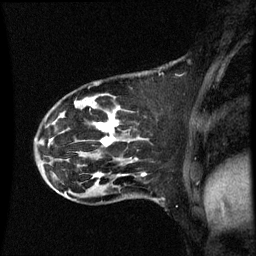
Breast MRI (dynamic contrast-enhanced), one sagittal slice. Slice 18 of 60 in the series (ordered by position). Dynamic contrast-enhanced series, image 2 of 3 at this slice position (ordered by acquisition). 1.5 T. TE 4.2 ms, TR 8.9 ms. 2 mm slice thickness. 256 × 256 image matrix, field of view 200 × 200 mm. Female patient, age 44 years. From the clinical record (not read from this slice): setting: breast cancer imaged before/during neoadjuvant chemotherapy; receptor status: HR-positive, HER2-negative.
Outlined on this slice (semi-automatic segmentation, software-assisted and operator-edited):
- analysis volume of interest (the breast-tissue region the enhancement analysis was run in; not a lesion): bounding box <43,82,149,189> (left, top, right, bottom; pixels)
- tumour enhancement mask (voxels above the 70 % enhancement threshold inside the analysis volume of interest): <96,116,119,177>